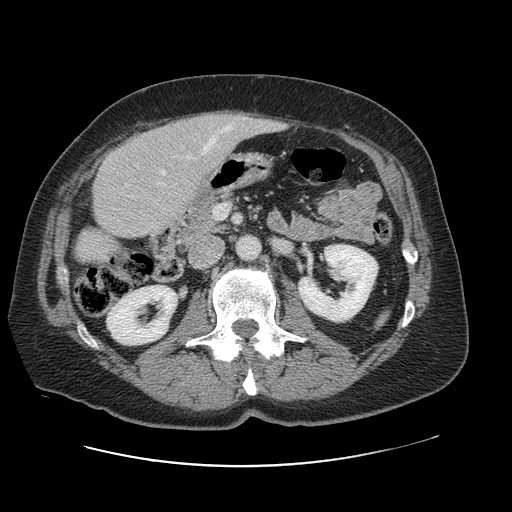
Contrast-enhanced abdominal CT, one axial slice. Slice 35 of 138 in the series (ordered by position). 120 kVp. Intravenous contrast given. Soft-tissue window (W 400 / L 40 HU). 2.5 mm slice thickness. 512 × 512 image matrix, field of view 402 × 402 mm. Male patient, age 71 years. From the clinical record (not read from this slice): diagnosis: colorectal cancer liver metastases, imaged before liver resection.
Structures marked on this image (manually delineated by an expert):
- hepatic veins: bounding box <202,125,231,155> (left, top, right, bottom; pixels)
- liver: <76,112,278,263>
- planned liver remnant (the part of the liver to remain after resection): <76,133,189,263>
- portal vein (with intrahepatic branches): <161,171,166,175>